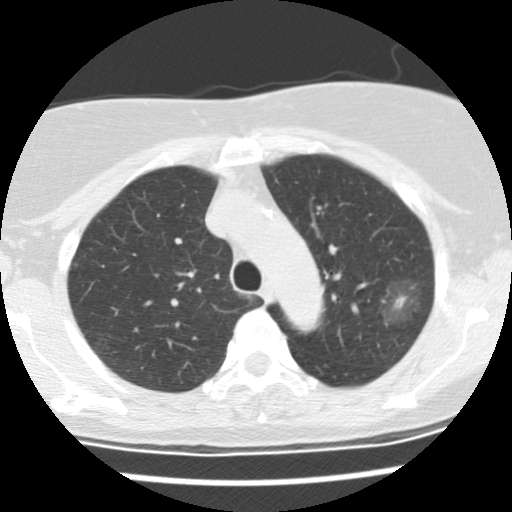
Axial slice from a low-dose chest CT screening exam. Baseline annual screen. Lung window (W 1500 / L -600 HU). Slice 106 of 137 in the series. Female, age 66 years at enrolment. Former smoker at enrolment.
• Expert reader's lesion annotation, bounding box <379,278,426,323> (left, top, right, bottom; pixels).
• Reader record for this screening exam (exam-level; its link to the box is not recorded): non-calcified nodule or mass ≥4 mm, left upper lobe, 25 × 17 mm, poorly defined margins, mixed attenuation.
• Participant outcome: lung cancer diagnosed 44 days after this screen — bronchiolo-alveolar adenocarcinoma, NOS, left upper lobe, well differentiated (G1), stage IA (AJCC 6th edition), 19 mm at pathology.